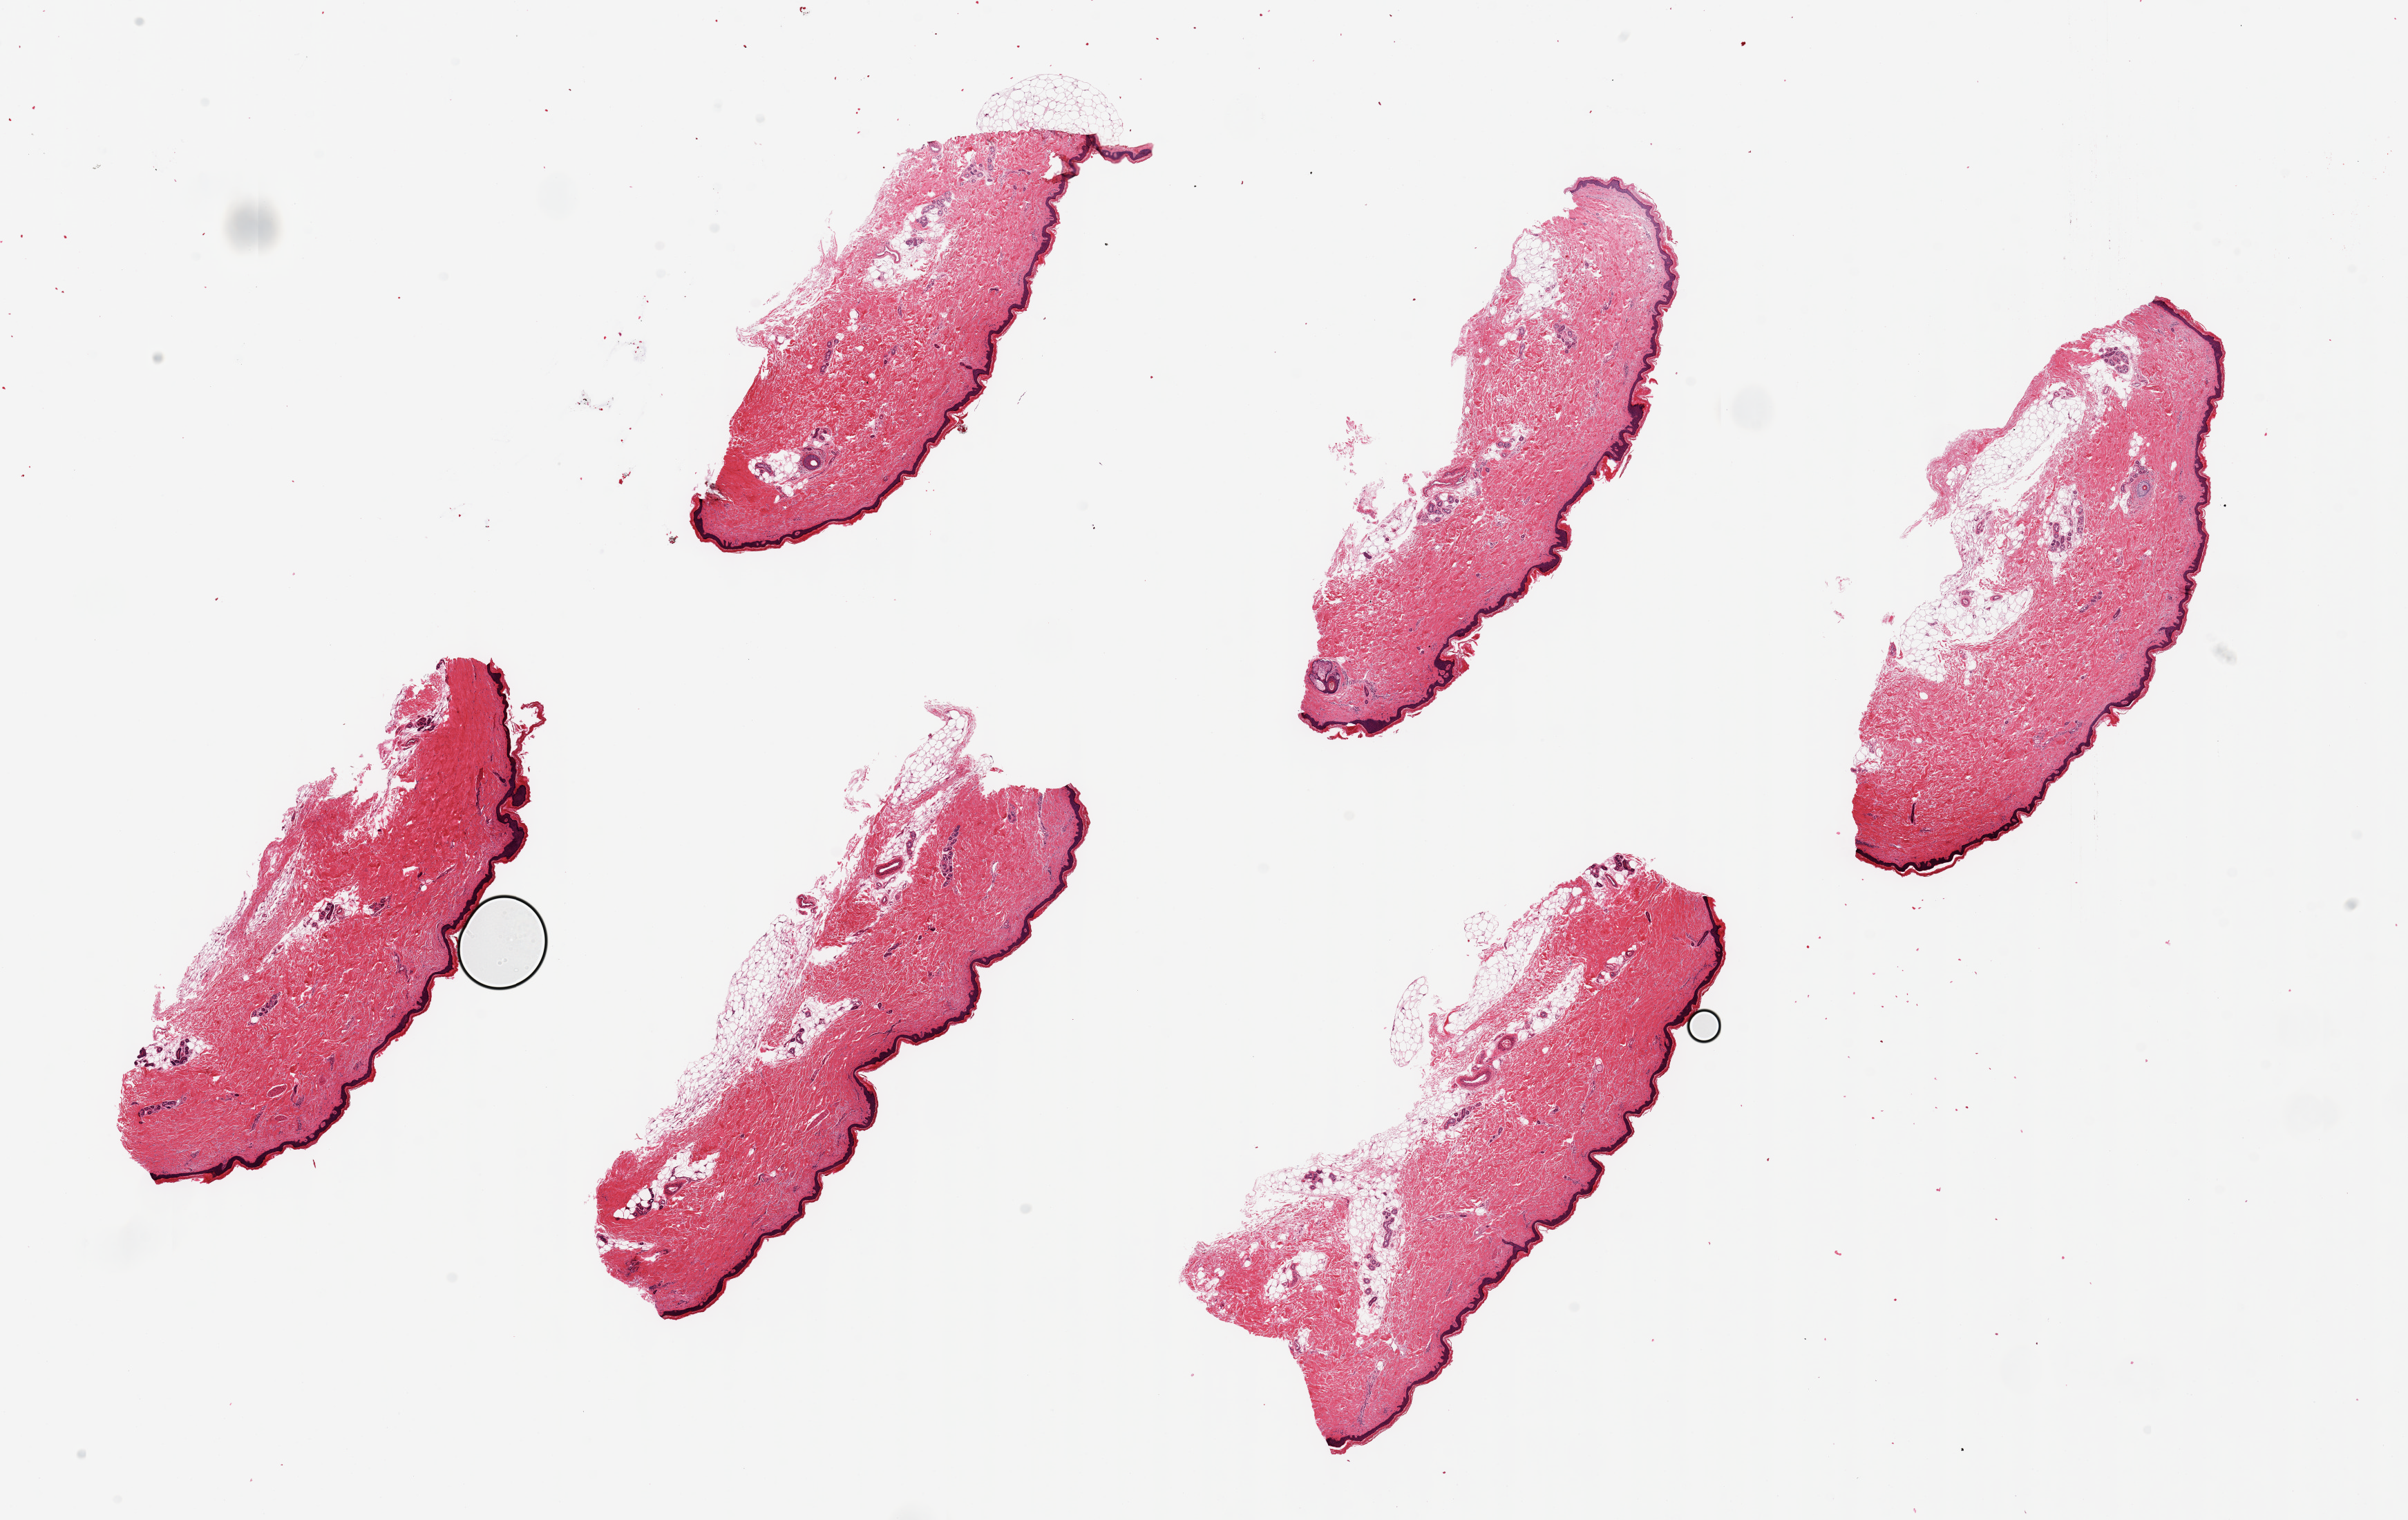
Haematoxylin and eosin whole-slide image — shown as a low-resolution overview of the whole scanned area (about 27.6 x 17.4 mm, acquisition: 20x scan); PAXgene-fixed, paraffin-embedded tissue; sampled site (target tissue): skin of lower leg; donor tissue sample.
Pathologist's review note for this sample: 6 pieces, up to 8x3mm; up to 0.5mm subcutaneous adipose.